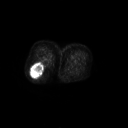
FDG PET of an extremity soft-tissue mass (from a PET/CT study), one axial slice; slice 34 of 267 in the series (ordered by position); 128 × 128 image matrix, field of view 700 × 700 mm. Patient: female, 70 years. Case-level facts recorded for this patient, not image findings: histological type: synovial sarcoma; grade: intermediate; site of the primary tumour: right buttock.
Annotated regions visible in this slice (expert contour drawn on MRI and transferred to this co-registered scan by the dataset authors):
- gross tumour volume including surrounding oedema: box from (x=30, y=61) to (x=43, y=77) px
- gross tumour volume (mass): (x=30, y=62)–(x=43, y=77)